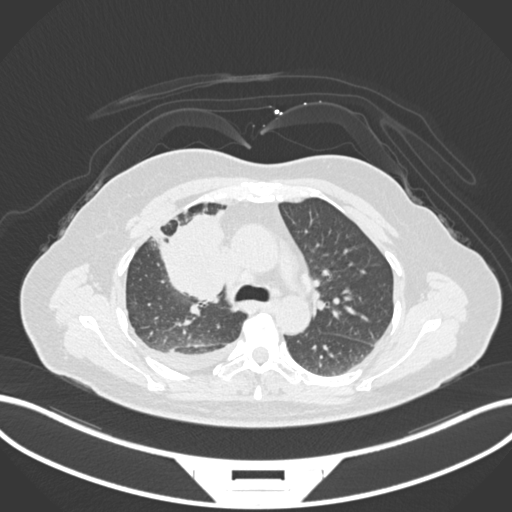
Chest CT, one axial slice; slice 102 of 172 in the series (ordered by position); 120 kVp; lung window (W 1500 / L -600 HU); 512 × 512 image matrix. Patient: female, 52 years. From the clinical record (not read from this slice): clinical TNM (as recorded): T3 N1 M1.
Outlined on this slice (rectangle marked by the reading radiologist):
- lung tumour (recorded histology: adenocarcinoma): bounding box <147,201,231,307> (left, top, right, bottom; pixels)